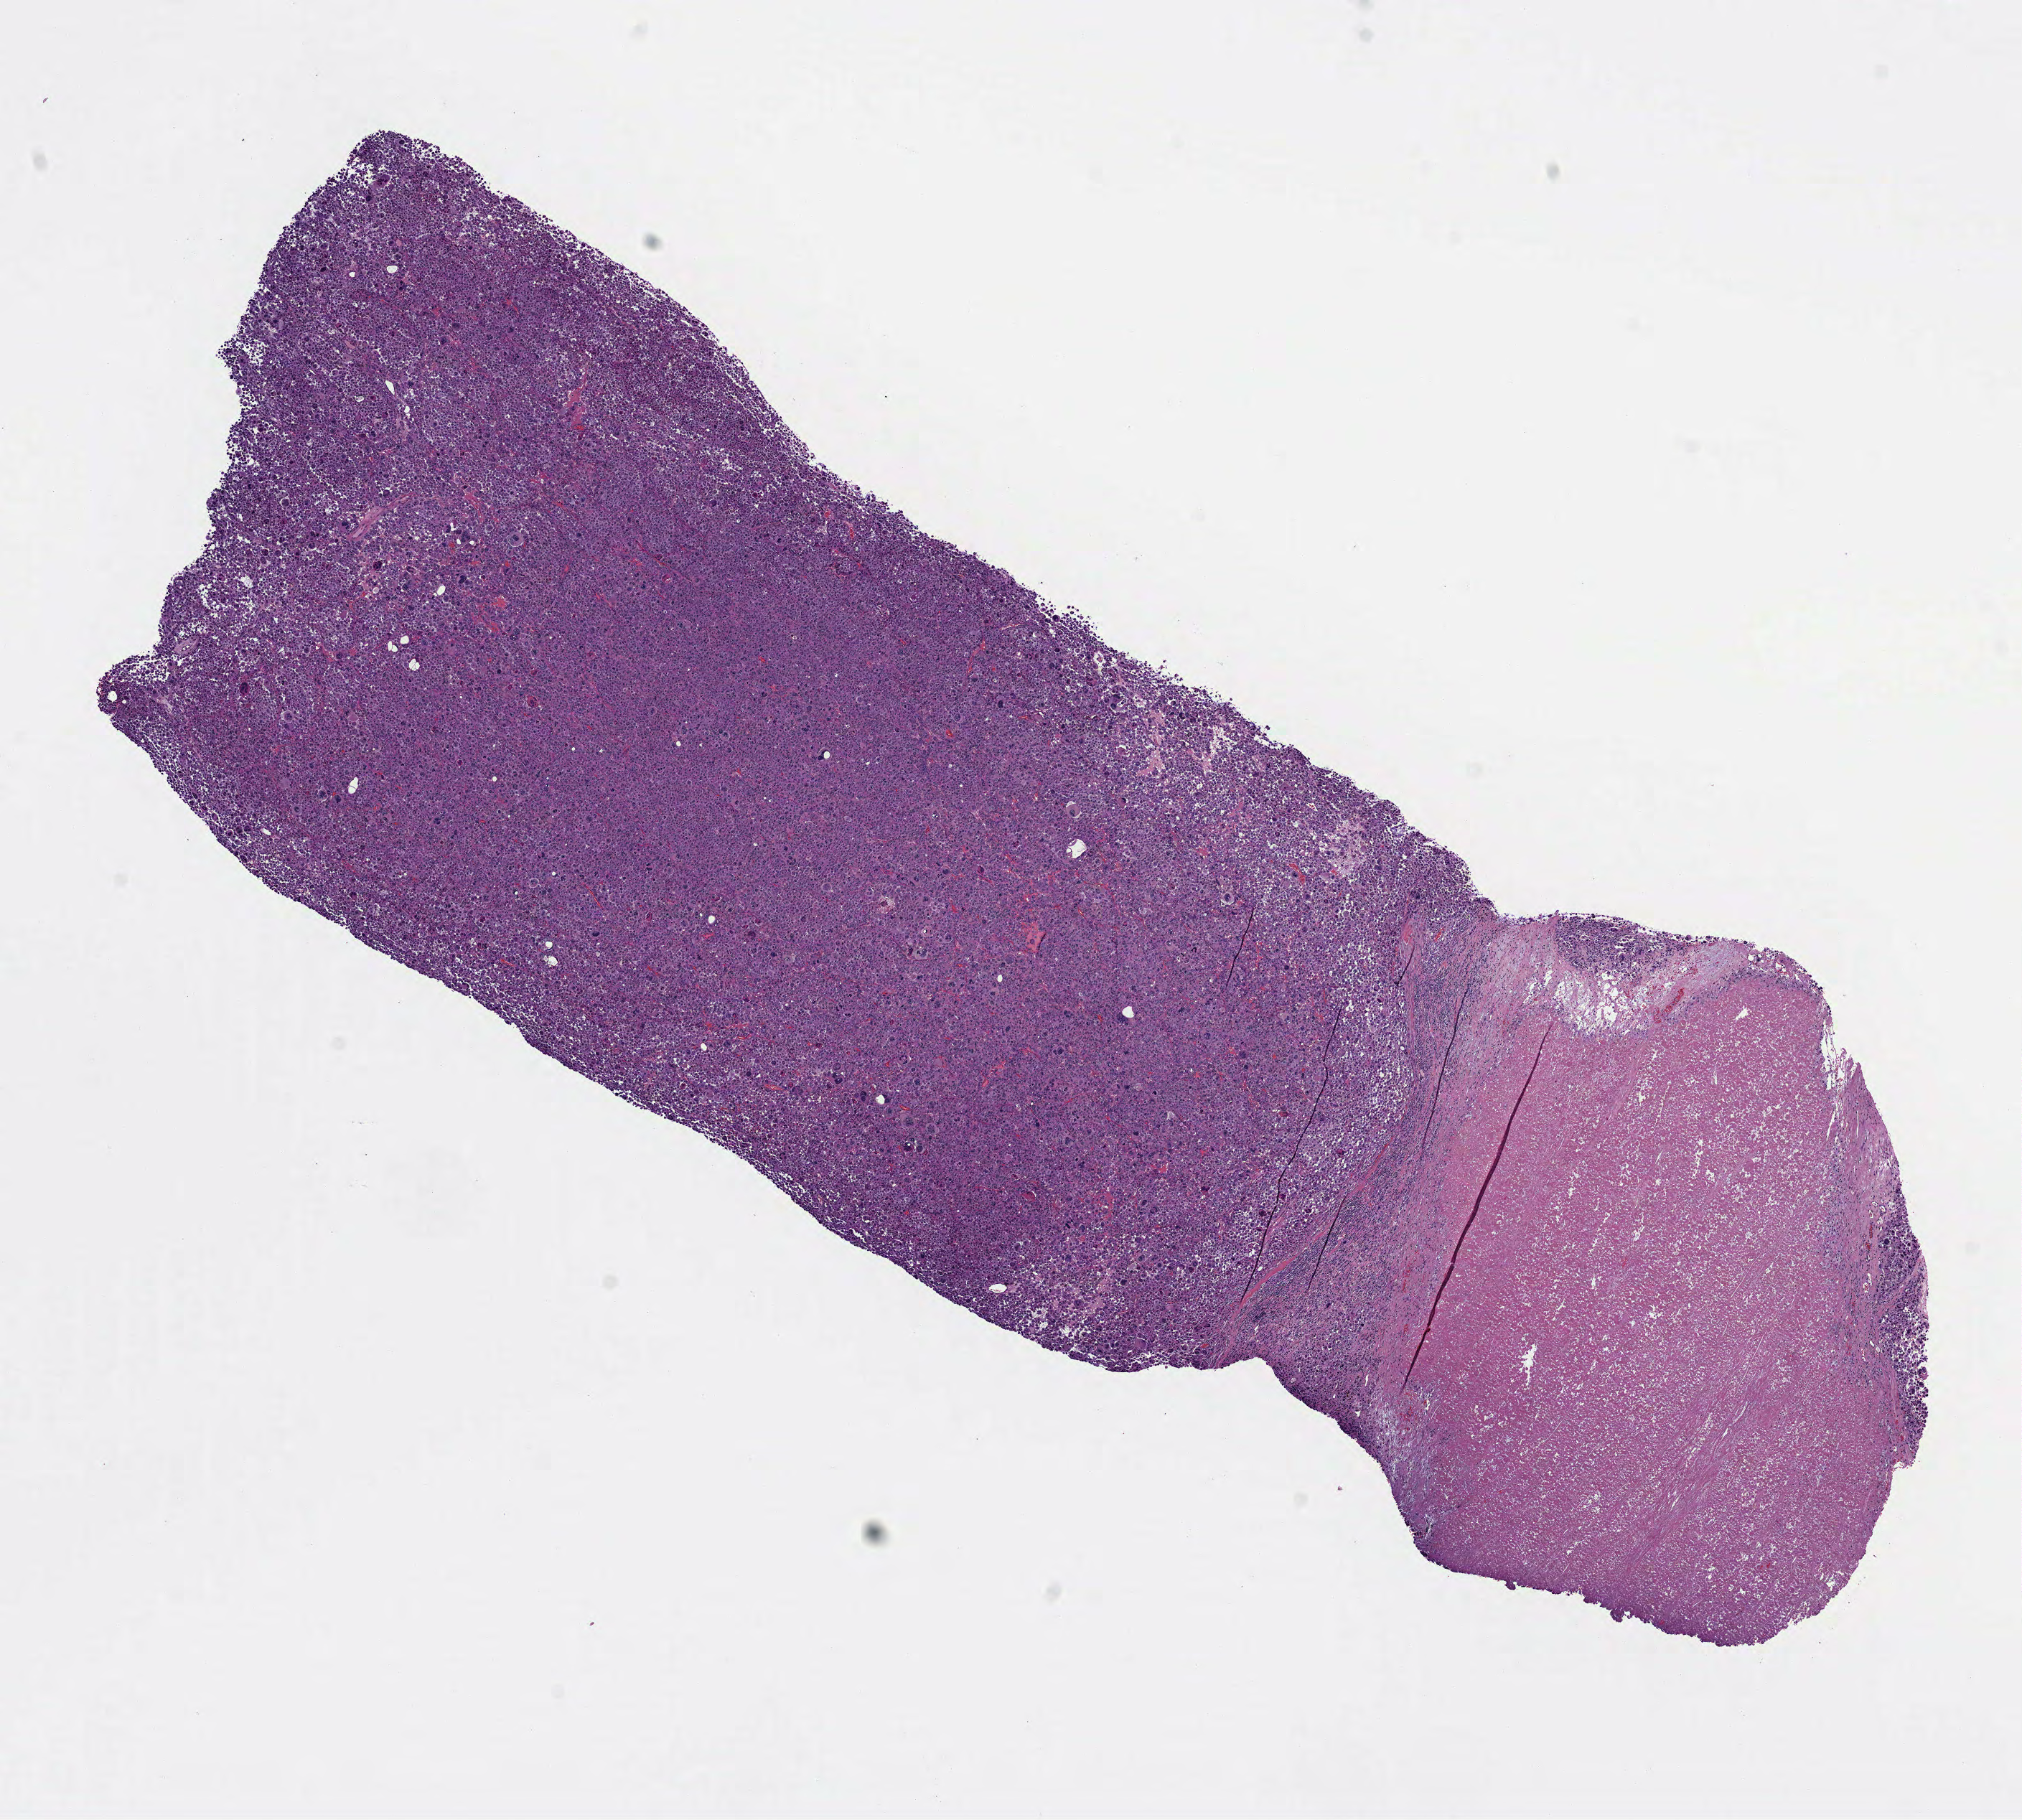
Hematoxylin and eosin (H&E) stained whole-slide image — low-resolution overview of the scanned area, about 11.4 x 10.2 mm (acquisition: 40x scan); formalin-fixed paraffin-embedded (FFPE) diagnostic section; primary tumour sample from the skin. Patient: male, age at initial diagnosis 71 years.
Pathologic diagnosis: Malignant melanoma, NOS.